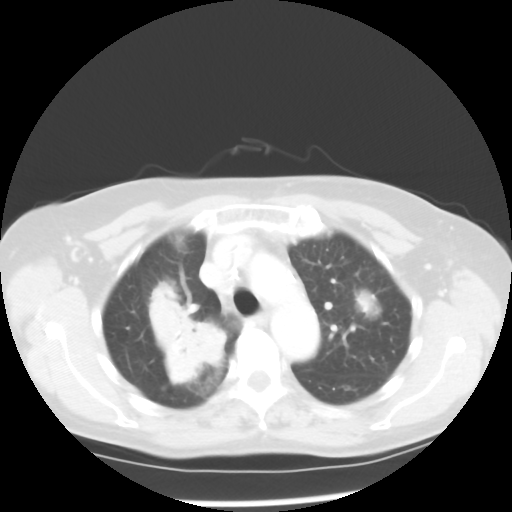
Chest CT, one axial slice. Position 38 of 52 along the scan axis. Reconstruction kernel STANDARD. 100 kVp. Lung window (W 1500 / L -600 HU). 5 mm slice thickness. 512 × 512 image matrix, field of view 328 × 328 mm. Patient: female, 60 years. Case-level facts recorded for this patient, not image findings: clinical TNM (as recorded): T2 N1 M1a.
Structures marked on this image (rectangle marked by the reading radiologist):
- lung tumour (recorded histology: adenocarcinoma): bounding box <142,282,231,389> (left, top, right, bottom; pixels)